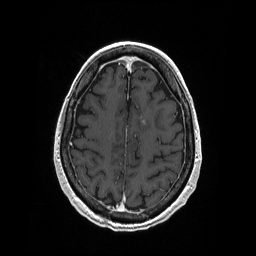
Brain MRI from a brain-tumour surgery series, one axial slice; position 66 of 208 along the scan axis; T1-weighted post-contrast; 1 mm slice thickness; 256 × 256 image matrix, field of view 256 × 256 mm. Case-level facts recorded for this patient, not image findings: histopathology: Primary diffuse large B-cell lymphoma; tumour location: Left Corpus Callosum (Frontal).
Annotated regions visible in this slice (expert manual segmentation):
- tumour: bounding box <142,120,146,126> (left, top, right, bottom; pixels)